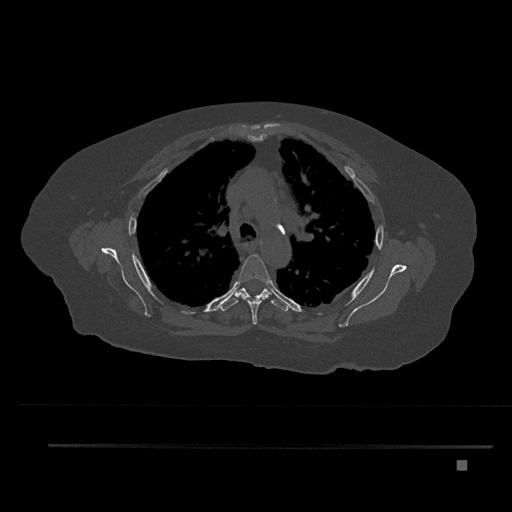
CT including the spine, one axial slice; position 588 of 797 along the scan axis; reconstruction kernel Br40s/3; 120 kVp; bone window (W 1800 / L 400 HU); 0.5 mm slice thickness; 512 × 512 image matrix, field of view 437 × 437 mm. Patient: female, 76 years. From the clinical record (not read from this slice): primary cancer: lung; vertebrae with lytic lesions (as recorded): T11, L3.
Outlined on this slice (semi-automatic segmentation, software-assisted and operator-edited):
- T4 vertebra: bounding box (x1, y1, x2, y2) in pixels: (236, 254, 271, 325)
- T5 vertebra: (219, 282, 289, 312)